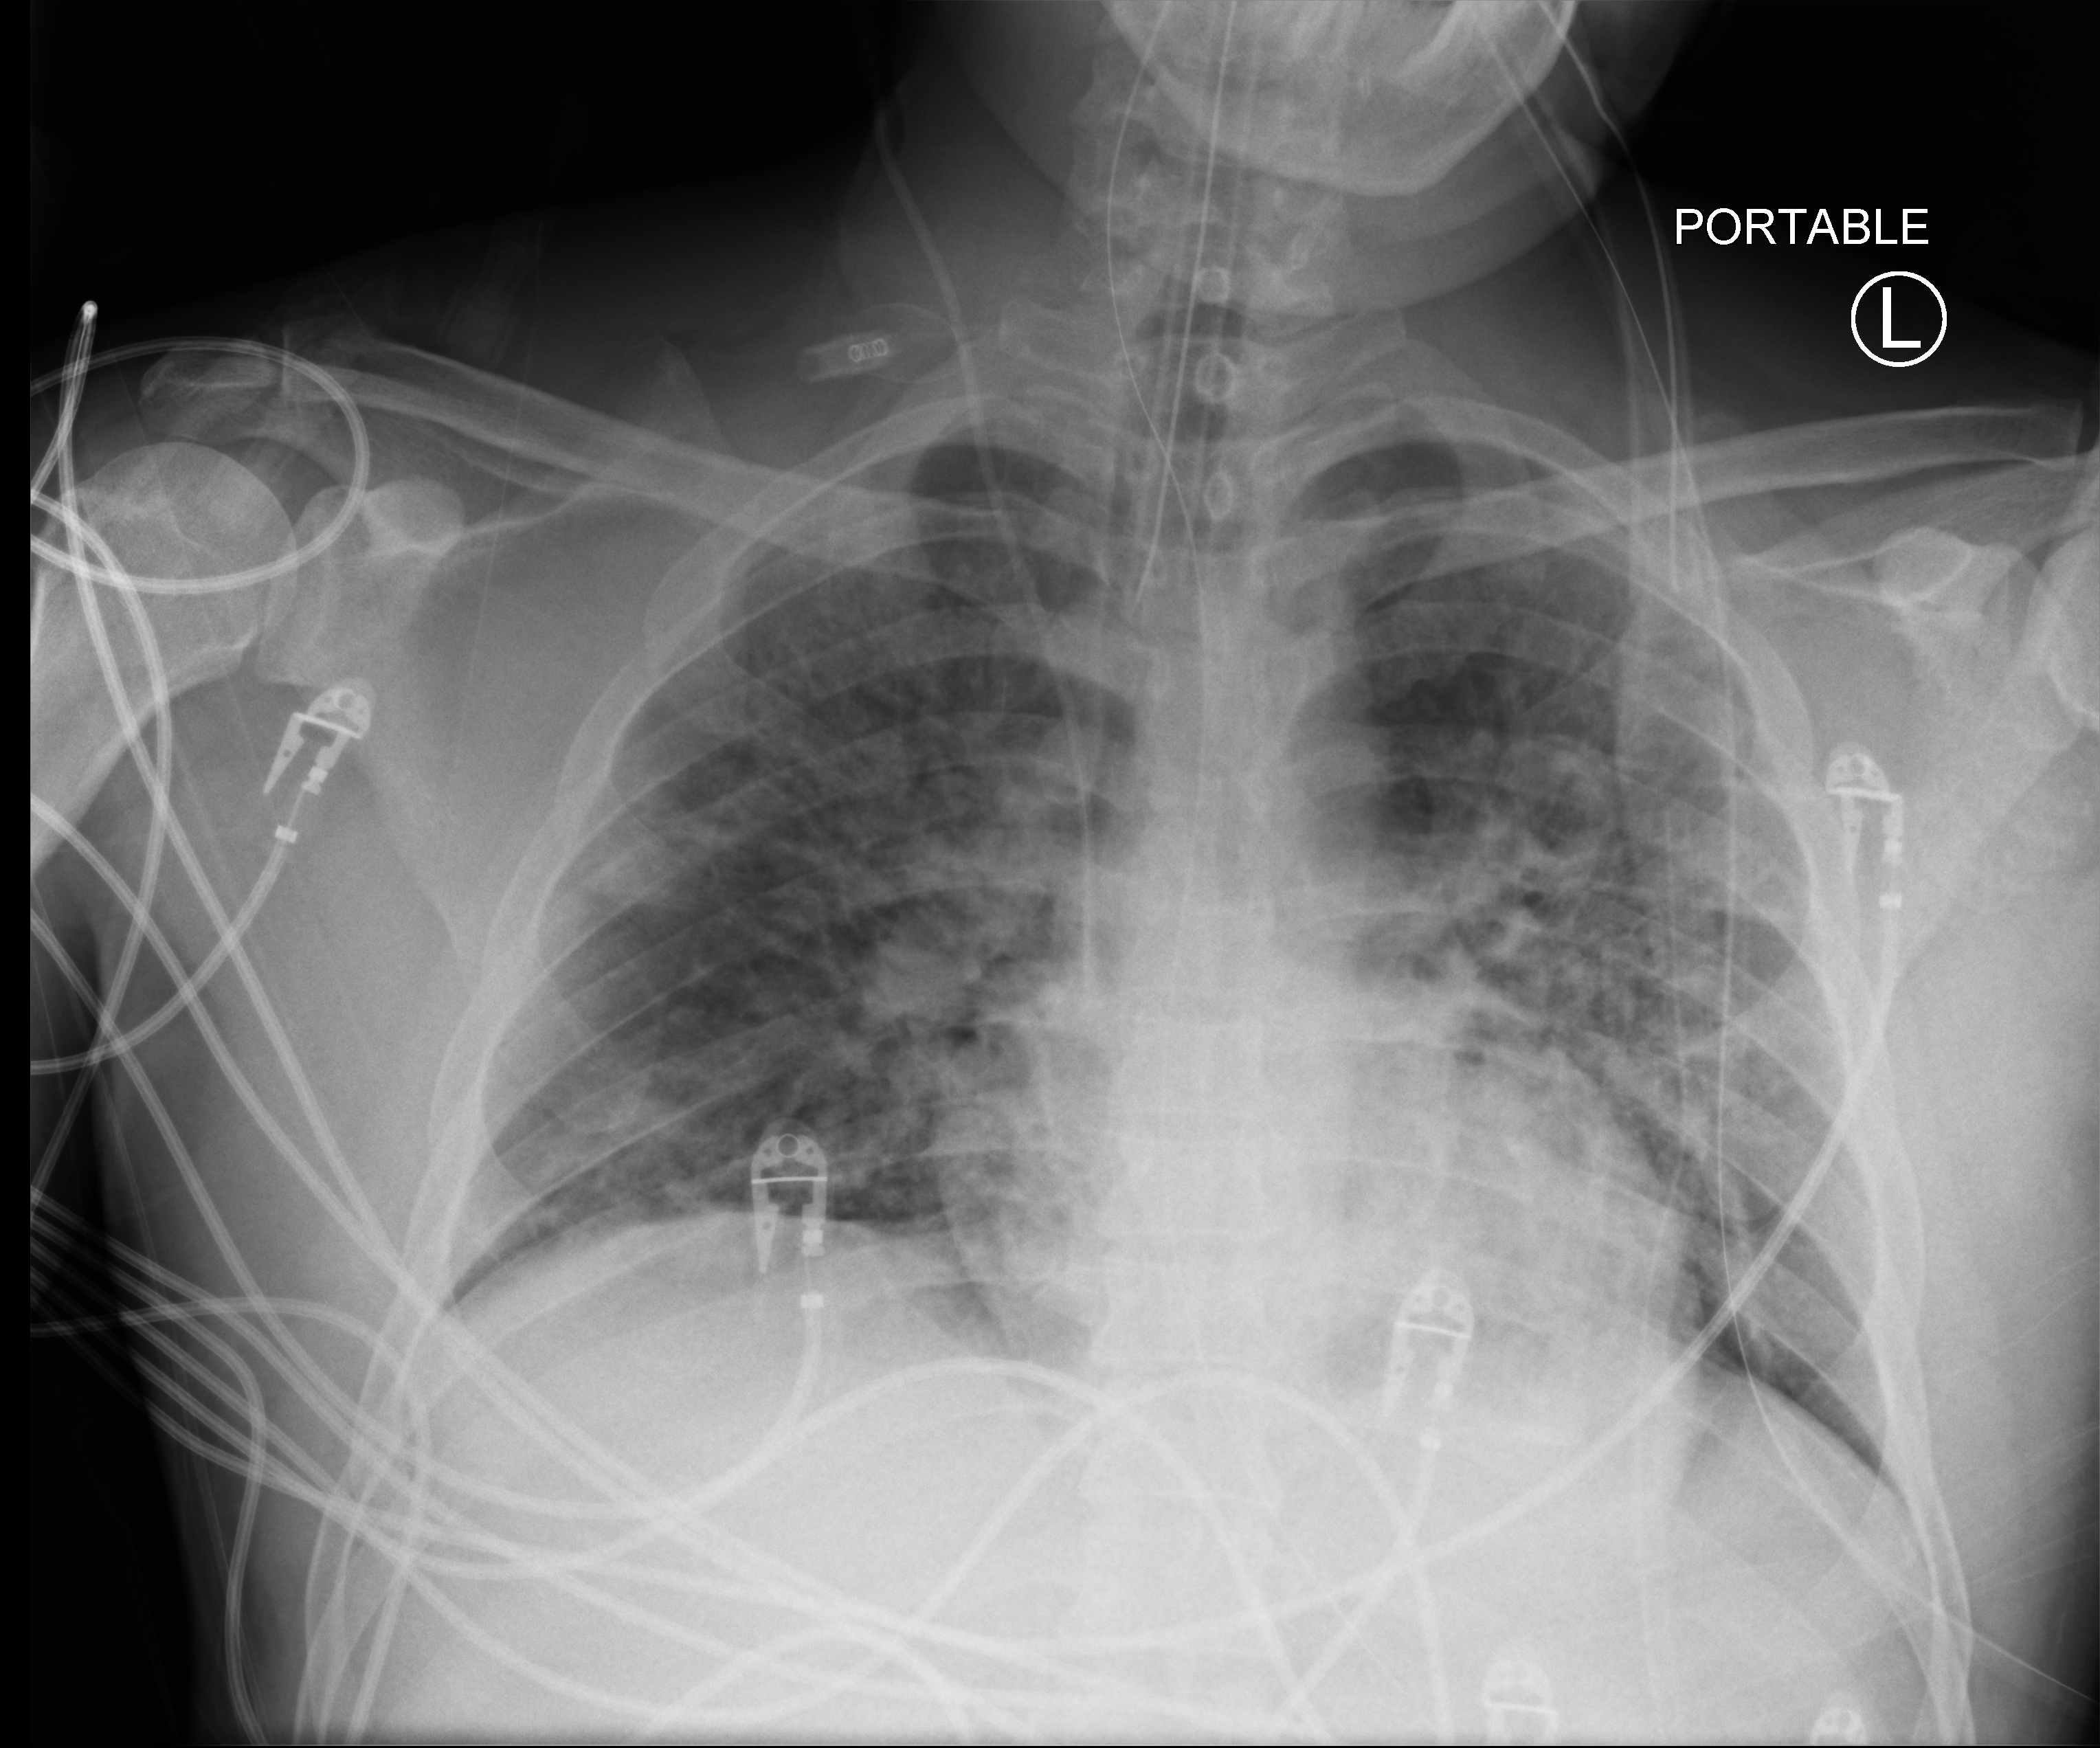
Bedside chest radiograph (computed radiography); anteroposterior (AP) projection. Male patient hospitalised with COVID-19, age 18–59 years.
From the hospital-stay record, not from the radiograph (when in the stay this image was taken is not recorded):
- diabetes (admission record): no
- admitted to intensive care during this hospital stay: yes
- mechanically ventilated during this hospital stay: yes